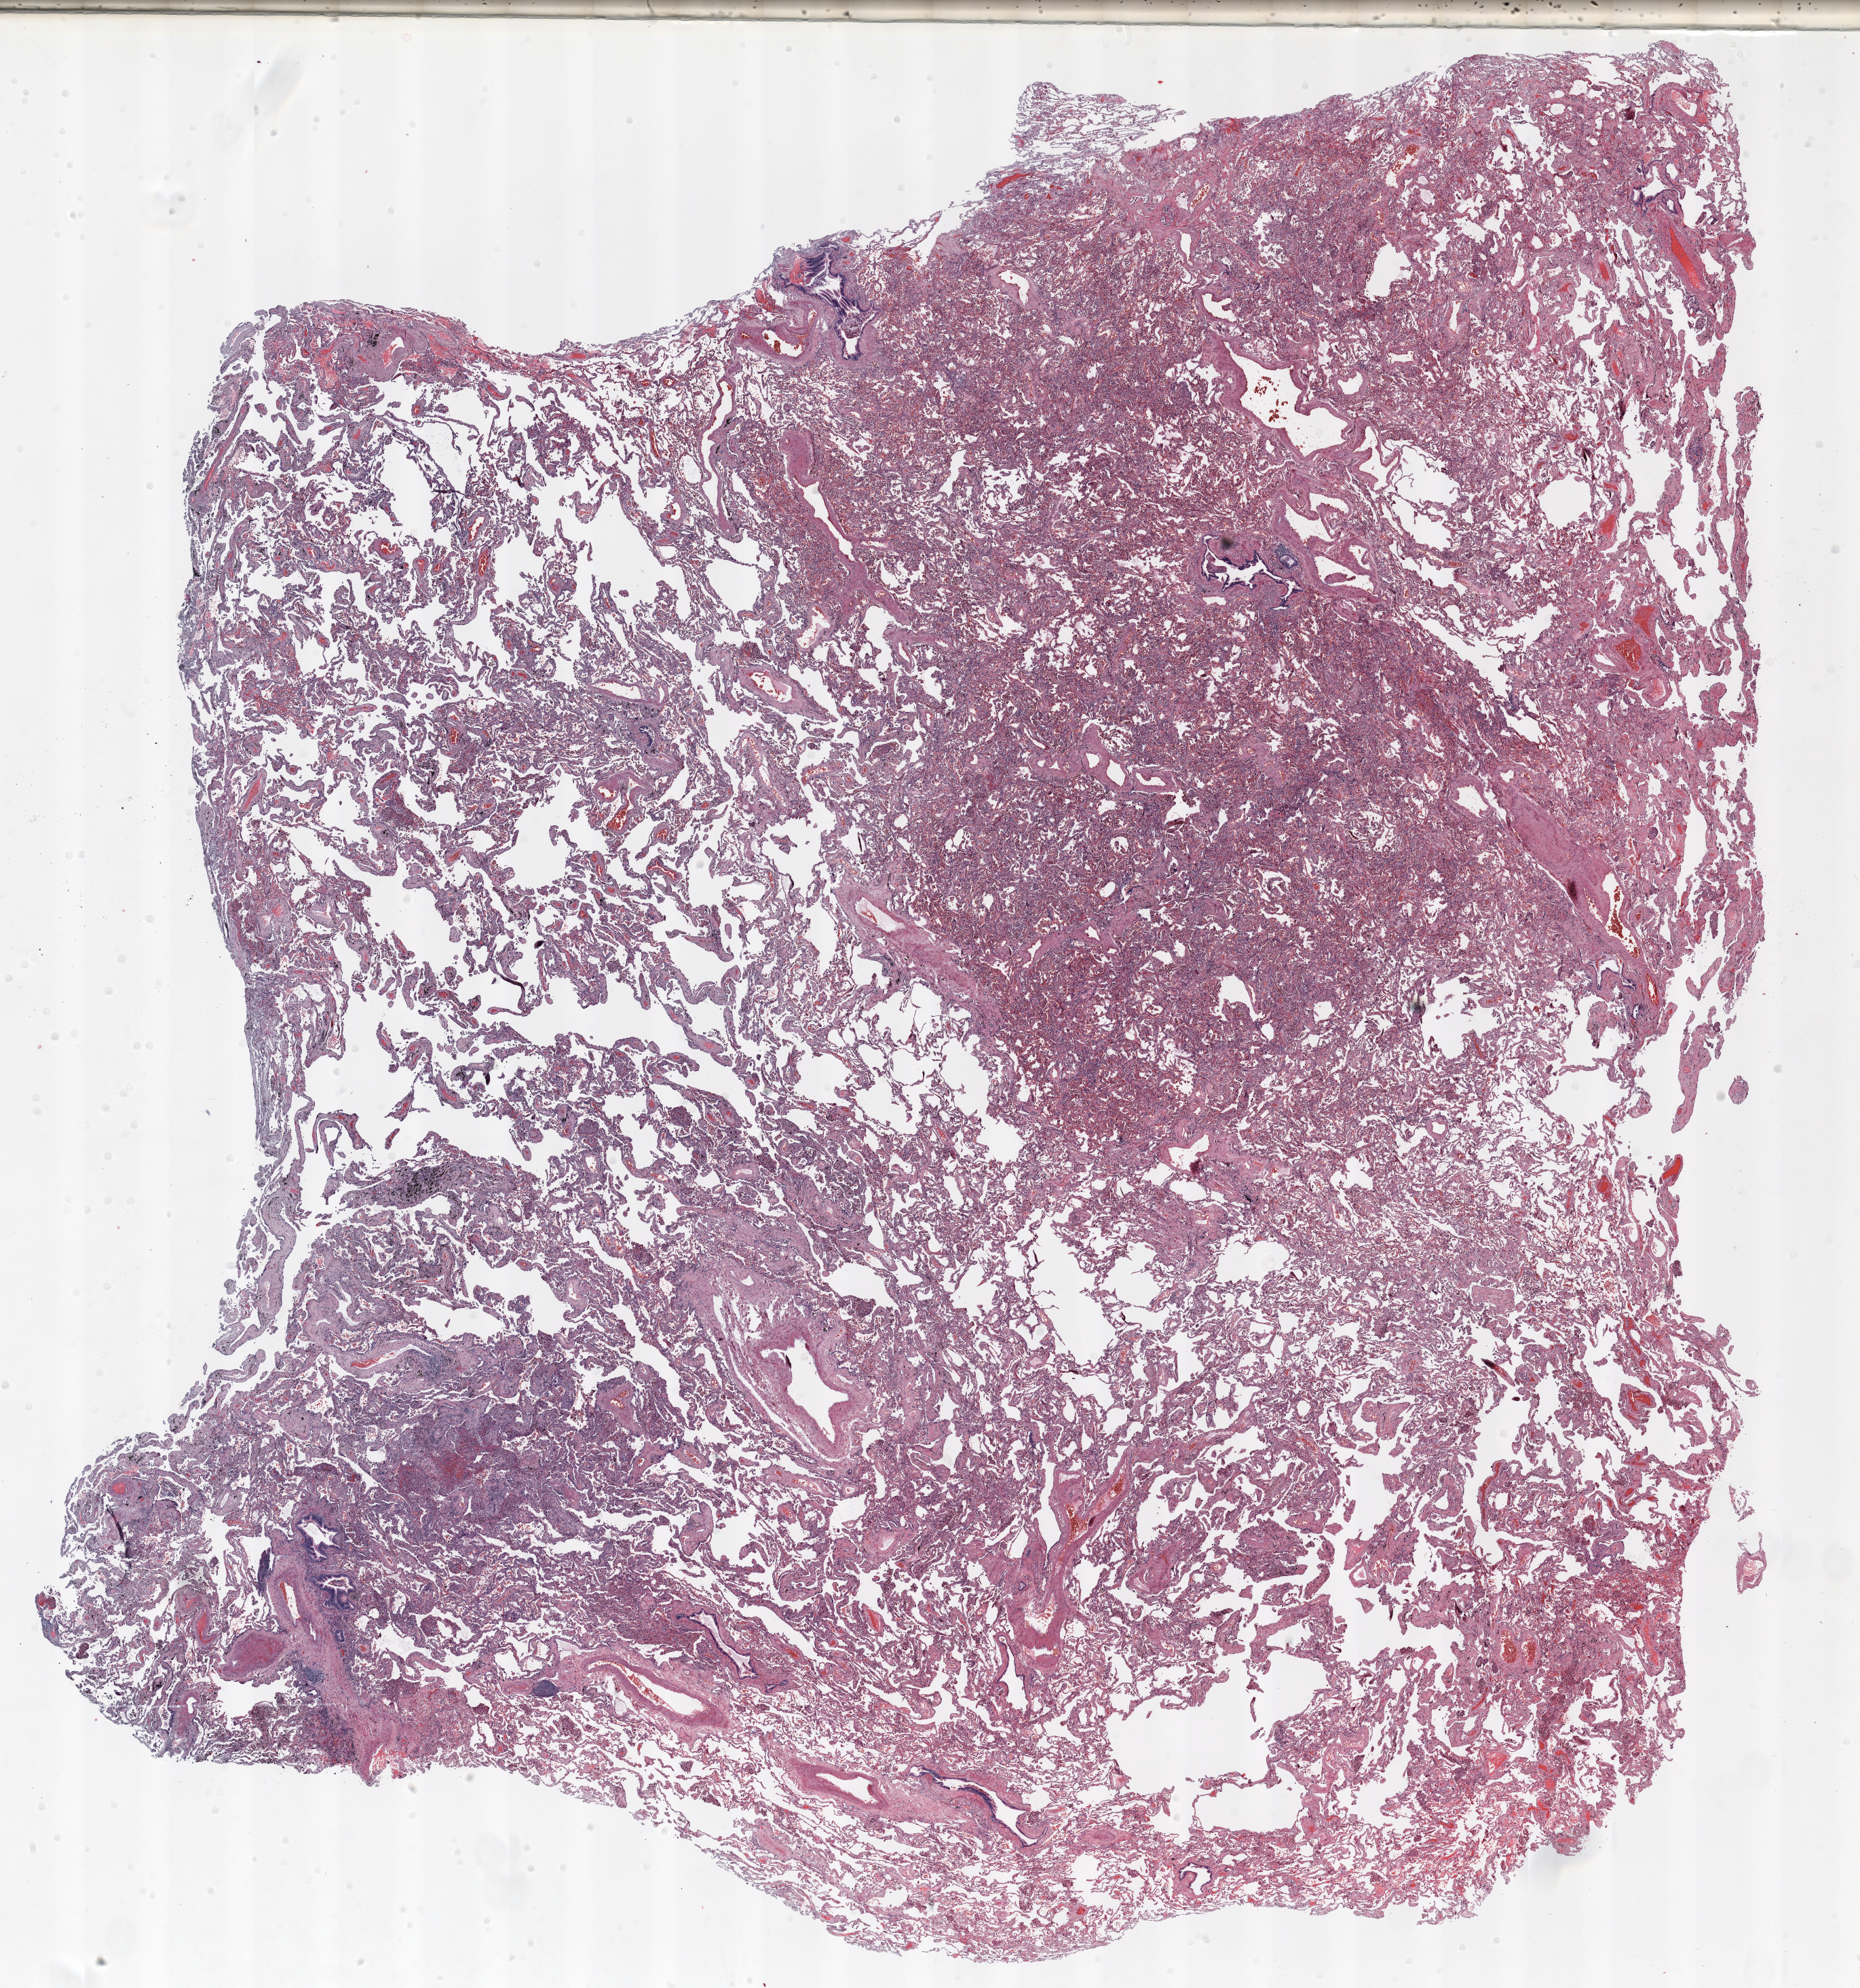
Whole-slide histology image, H&E, a low-resolution overview of the entire scanned area, about 22.0 x 23.5 mm (acquisition: 20x scan). FFPE section. Lung. Female, age 60 at enrolment. Current smoker at enrolment. Grade: moderately differentiated (G2).
Participant's lung-cancer diagnosis: Squamous cell carcinoma, keratinizing, NOS. Primary tumour location (clinical record): right upper lobe. Stage (AJCC 6th edition): IA. Tumour size (pathology): 20 mm. Note: participant had 2 primary lung cancers recorded; fields above describe the first.